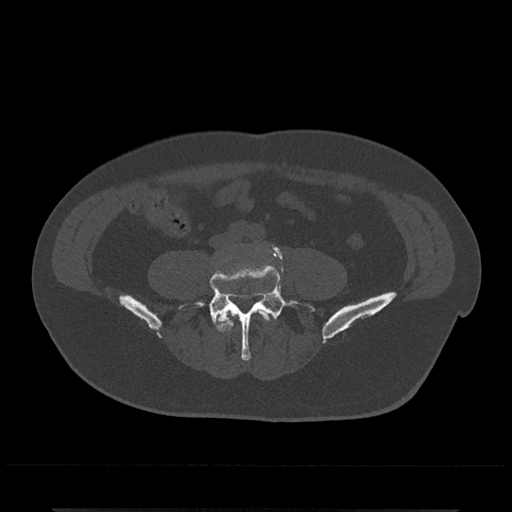
CT including the spine, one axial slice; position 104 of 797 along the scan axis; 120 kVp; bone window (W 1800 / L 400 HU); 512 × 512 image matrix, field of view 393 × 393 mm. Male patient, age 67 years. From the clinical record (not read from this slice): primary cancer: prostate.
Outlined on this slice (semi-automatically segmented with operator editing):
- L4 vertebra: bounding box <217,310,271,332> (left, top, right, bottom; pixels)
- L5 vertebra: <179,247,315,361>